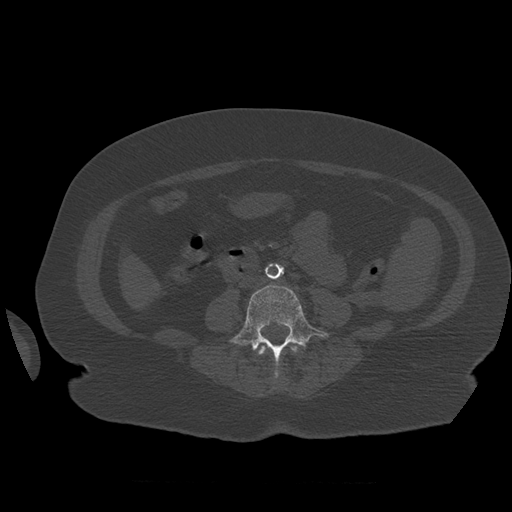
CT including the spine, one axial slice. Position 209 of 399 along the scan axis. Reconstruction kernel STANDARD. Bone window (W 1800 / L 400 HU). 512 × 512 image matrix, field of view 404 × 404 mm. Patient age 81 years. Case-level facts recorded for this patient, not image findings: primary cancer: renal.
Outlined on this slice (semi-automatically segmented with operator editing):
- L3 vertebra: bounding box <259,344,301,356> (left, top, right, bottom; pixels)
- L4 vertebra: <230,285,329,378>